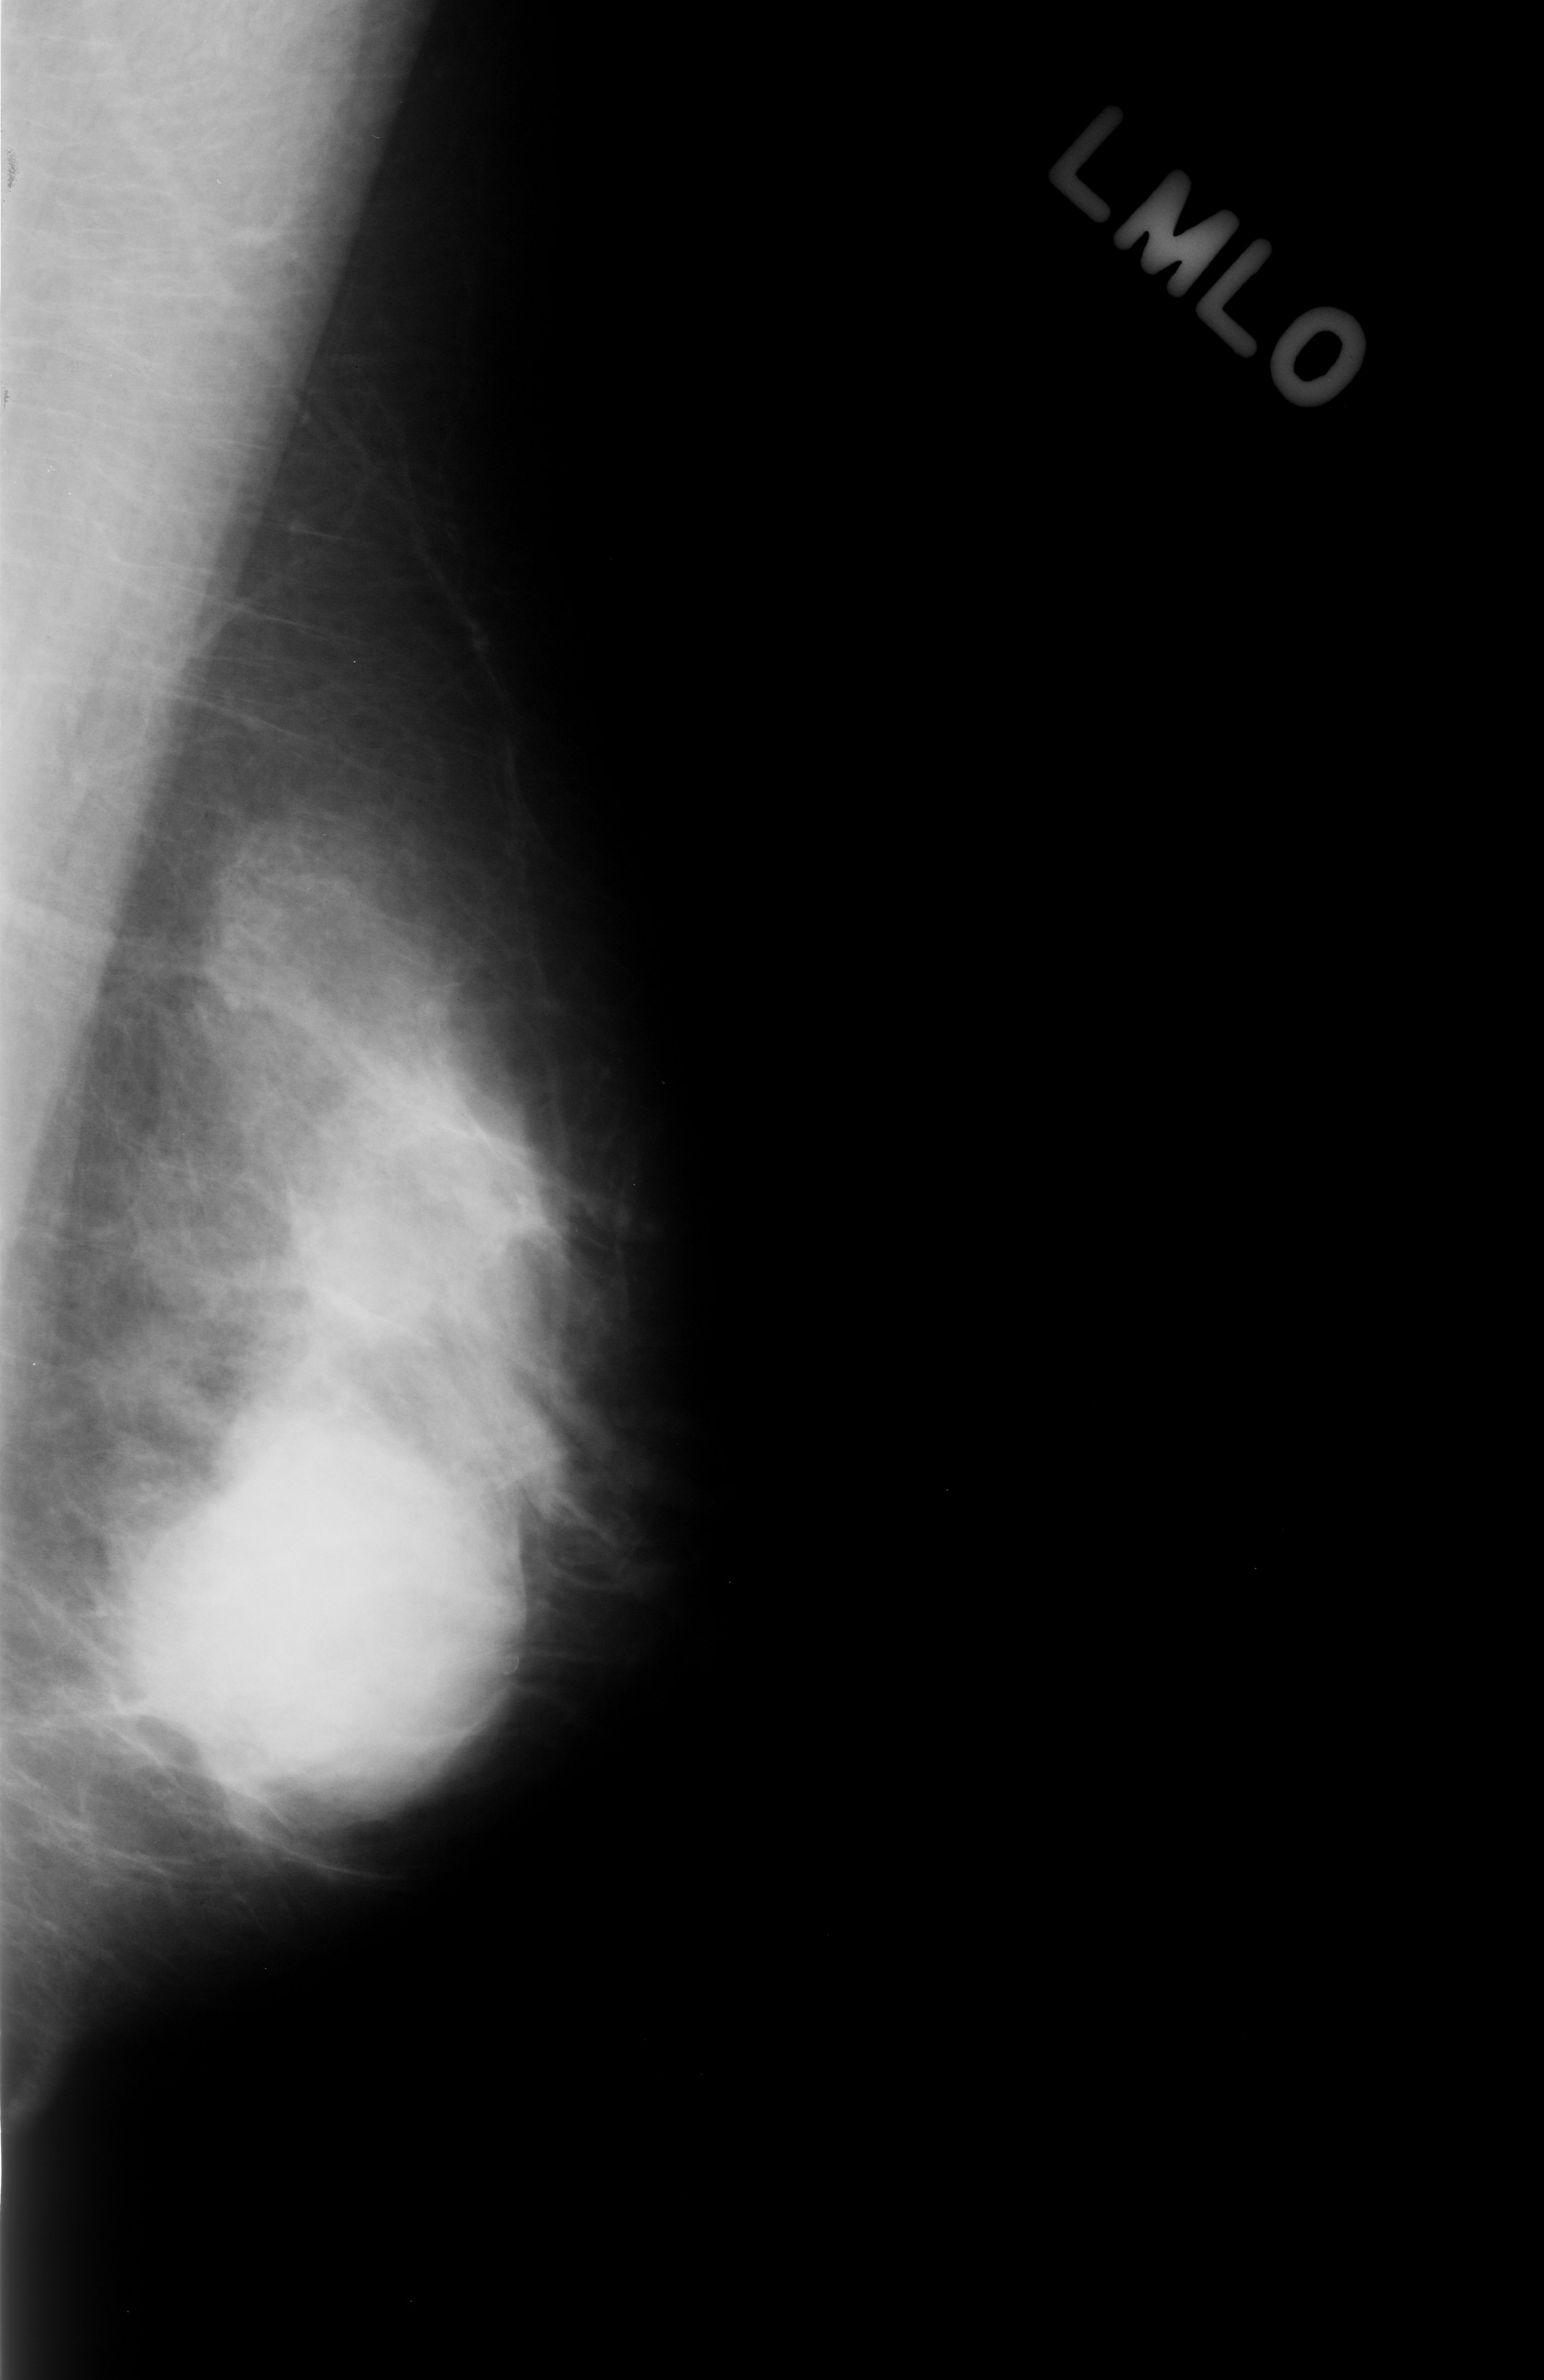
Mammogram (digitized film); left breast; mediolateral oblique (MLO) view; BI-RADS breast density category 4 (scale 1–4); 1544 × 2380 image matrix.
Marked abnormalities (boxes around the expert regions of interest):
- mass, shape round, margins obscured; BI-RADS assessment category 4; subtlety rating 5 on a 1 (subtle) to 5 (obvious) scale; pathology (as recorded): benign: box from (x=82, y=1438) to (x=551, y=1841) px